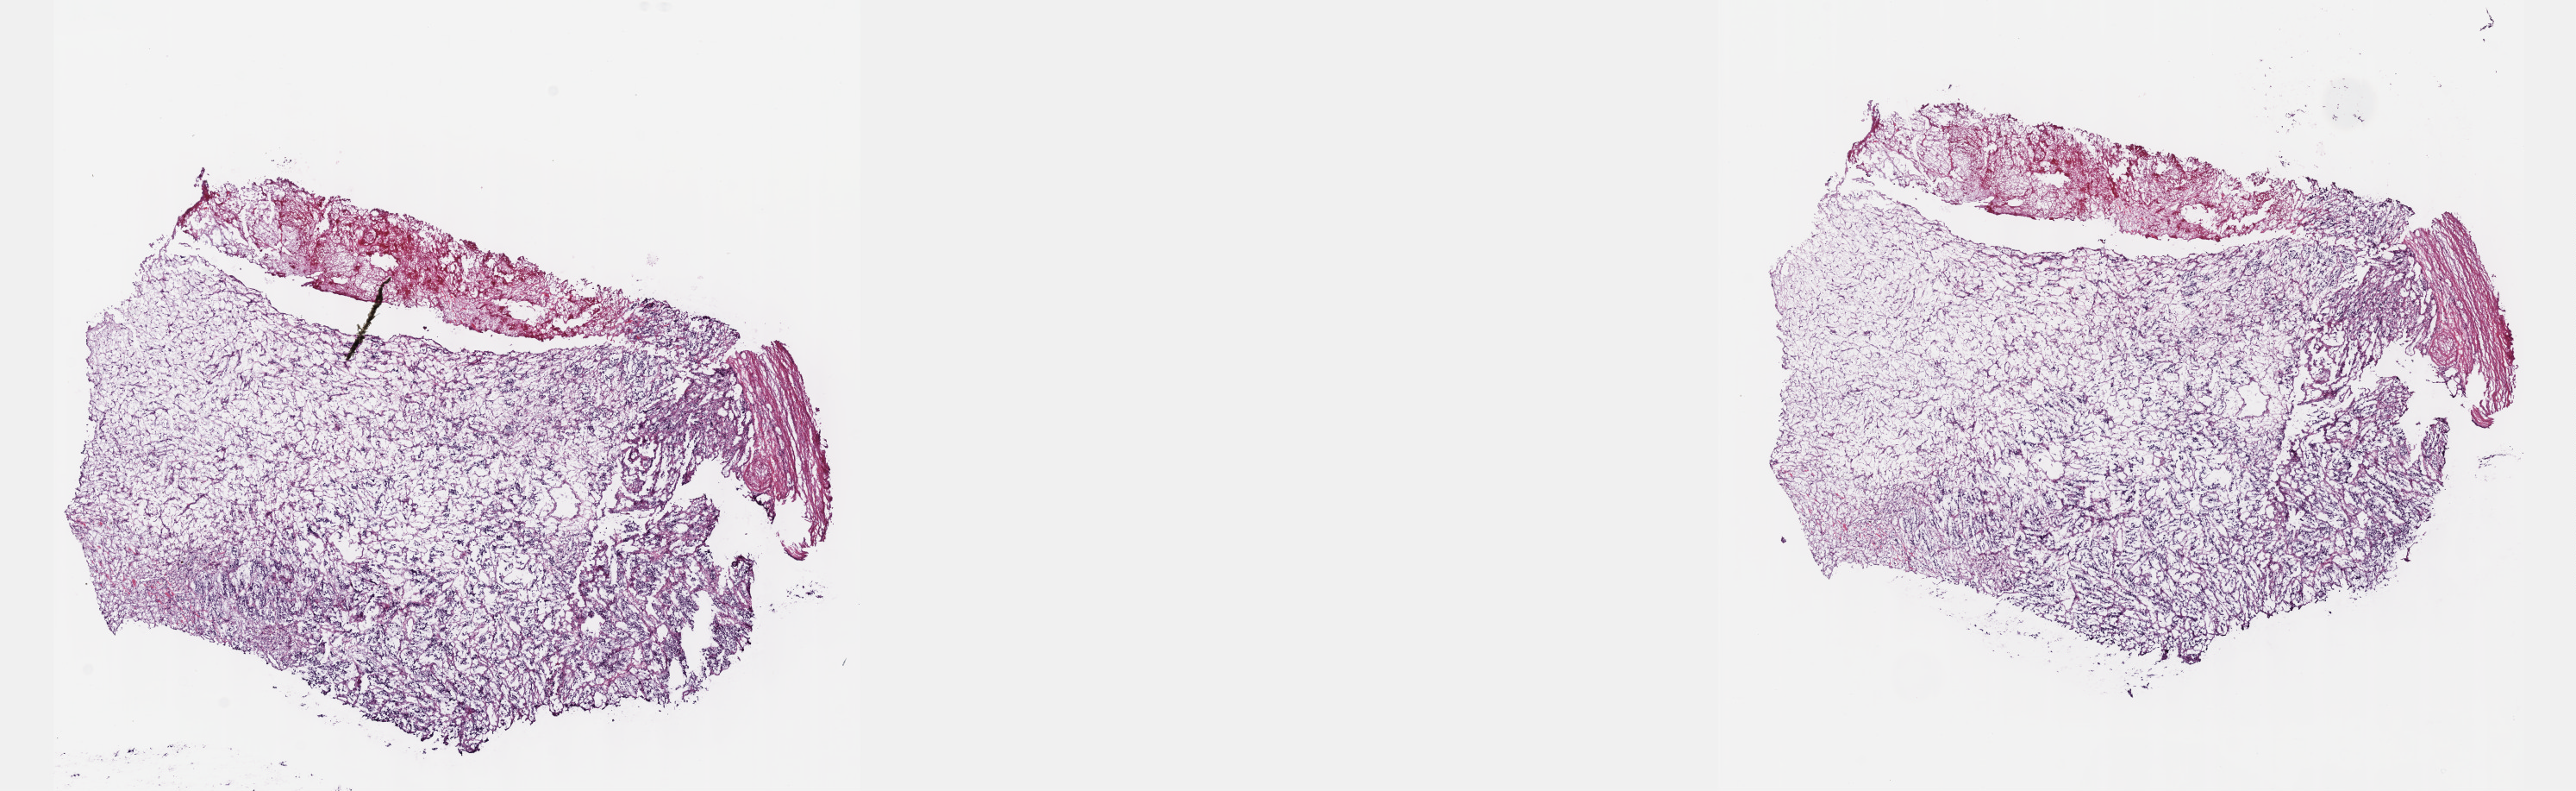
Digitized H&E-stained tissue section (whole slide) — shown as a low-resolution overview of the whole scanned area (about 24.1 x 7.4 mm); frozen section; primary tumour sample from the adrenal gland. Male patient; age at initial diagnosis 19 years. Composition of this section per pathologist review: tumour cells 90%, tumour nuclei 98%, normal cells 0%, stromal cells 10%, necrosis 0%. Infiltration values recorded for this section: lymphocyte infiltration 0%, monocyte infiltration 0%, neutrophil infiltration 0%.
* diagnosis: Pheochromocytoma, malignant